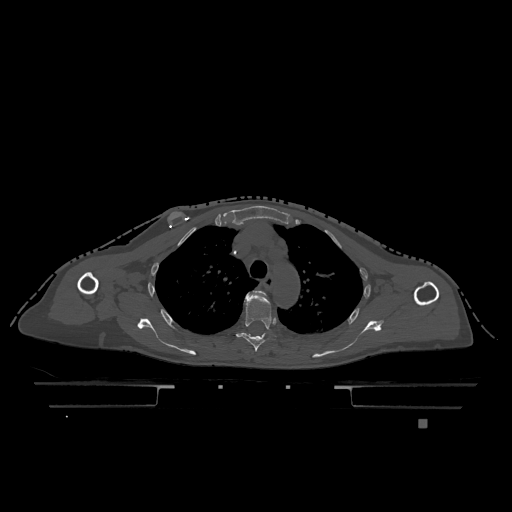
CT including the spine, one axial slice; position 882 of 1317 along the scan axis; bone window (W 1800 / L 400 HU); 0.5 mm slice thickness; 512 × 512 image matrix. Female patient, age 74 years. Case-level facts recorded for this patient, not image findings: primary cancer: lung.
Structures marked on this image (semi-automatically segmented with operator editing):
- T3 vertebra: bounding box (x1, y1, x2, y2) in pixels: (253, 291, 266, 298)
- T4 vertebra: (236, 292, 277, 352)